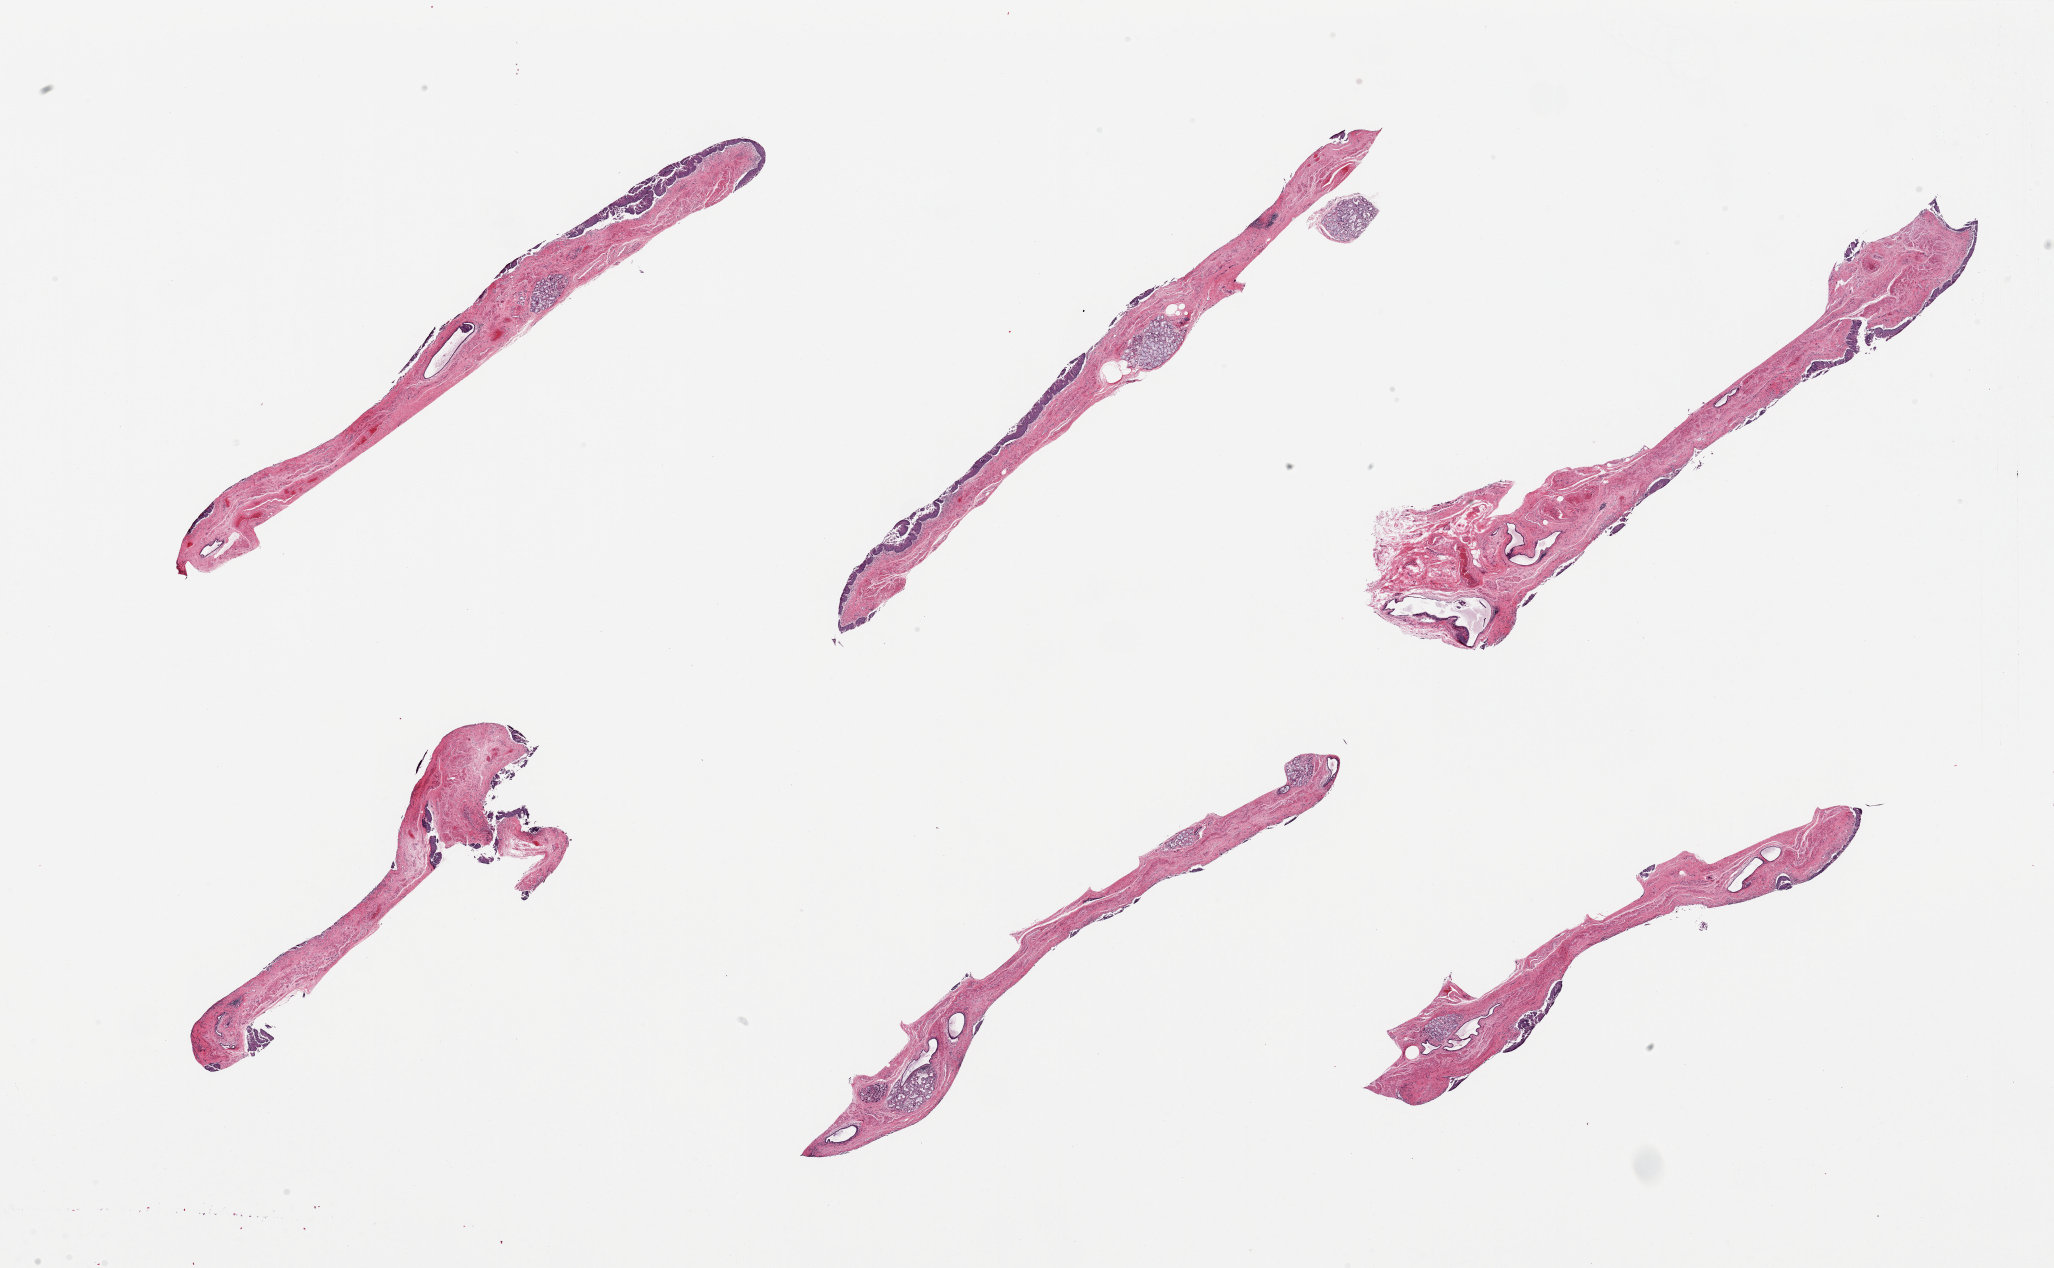
Hematoxylin and eosin (H&E) whole-slide image, brightfield — shown as a low-resolution overview of the whole scanned area (about 32.5 x 20.1 mm, acquisition: 20x scan); PAXgene-fixed, paraffin-embedded tissue; target tissue: esophageal mucous membrane; donor tissue sample. Donor: male.
Review note (as recorded): 6 pieces, unusually poorly preserved, squamous mucosa partly to in some areas totally sloughed, residual is ~50-100 microns thick.